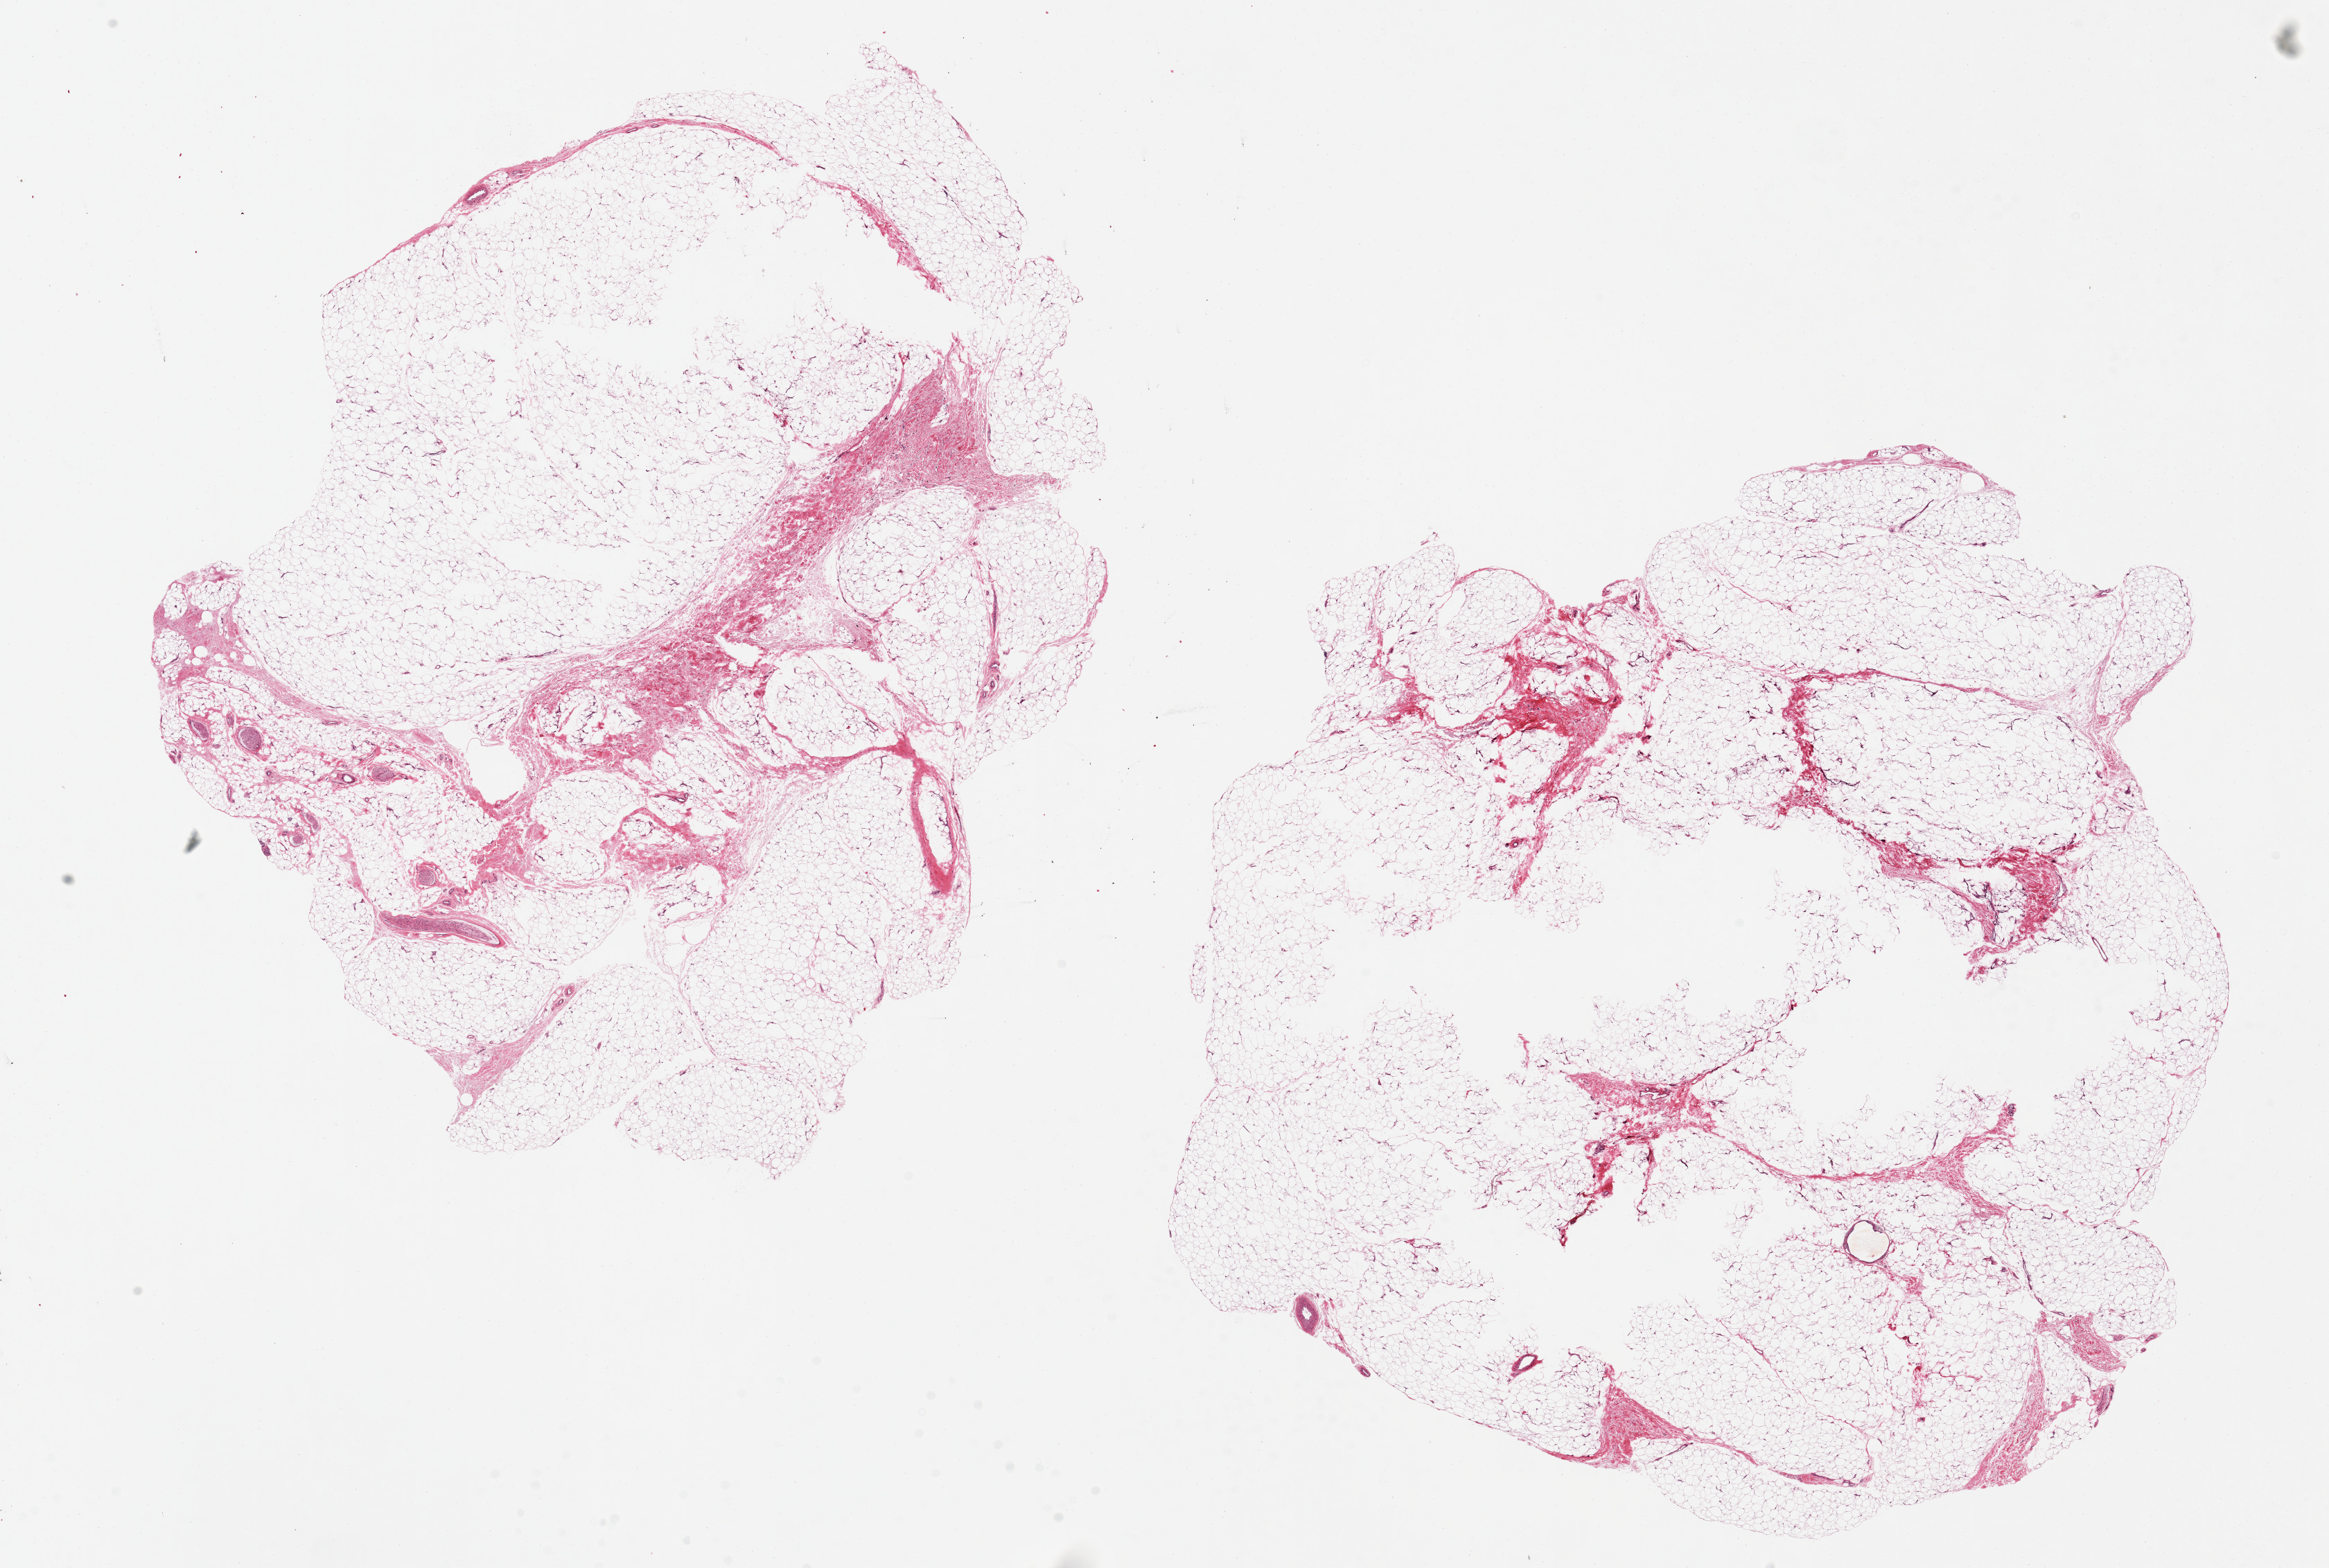
Digitized haematoxylin and eosin-stained section, shown as a low-resolution overview of the whole scanned area (about 26.6 x 17.9 mm, slide scanned at 20x). PAXgene-fixed paraffin-embedded (PFPE) section. Section of adipose tissue (target tissue). Tissue donor sample. Donor sex: female.
Review note (as recorded): 2 pieces. 12x11 & 12x12mm; Central holes.